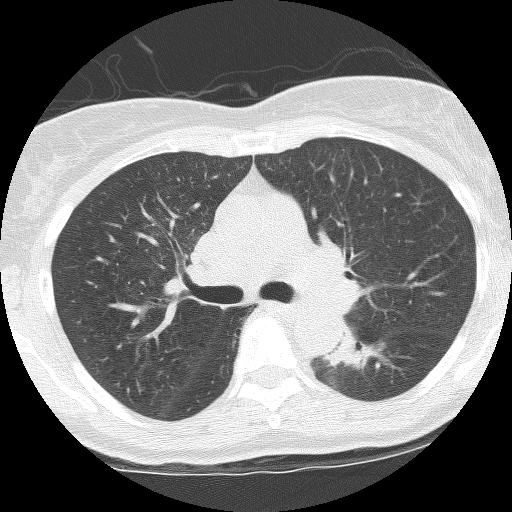
Low-dose screening chest CT, axial slice, third screening round (two years after baseline), lung window (W 1500 / L -600 HU), 2.5 mm slice thickness, lung (sharp) reconstruction kernel (BONE). Female participant, aged 62 years at enrolment. Former smoker at enrolment.
Expert-annotated lung lesion, box from (x=321, y=330) to (x=389, y=371) px. The screening reader recorded 3 non-calcified nodules or masses ≥4 mm on this exam (right upper lobe, left lower lobe, left upper lobe); which of them this box marks is not recorded. Official screen result: positive, other. Later outcome: lung cancer diagnosed 165 days after this screen — squamous cell carcinoma, NOS, left lower lobe, stage IIIB (AJCC 6th edition), 31 mm at pathology.